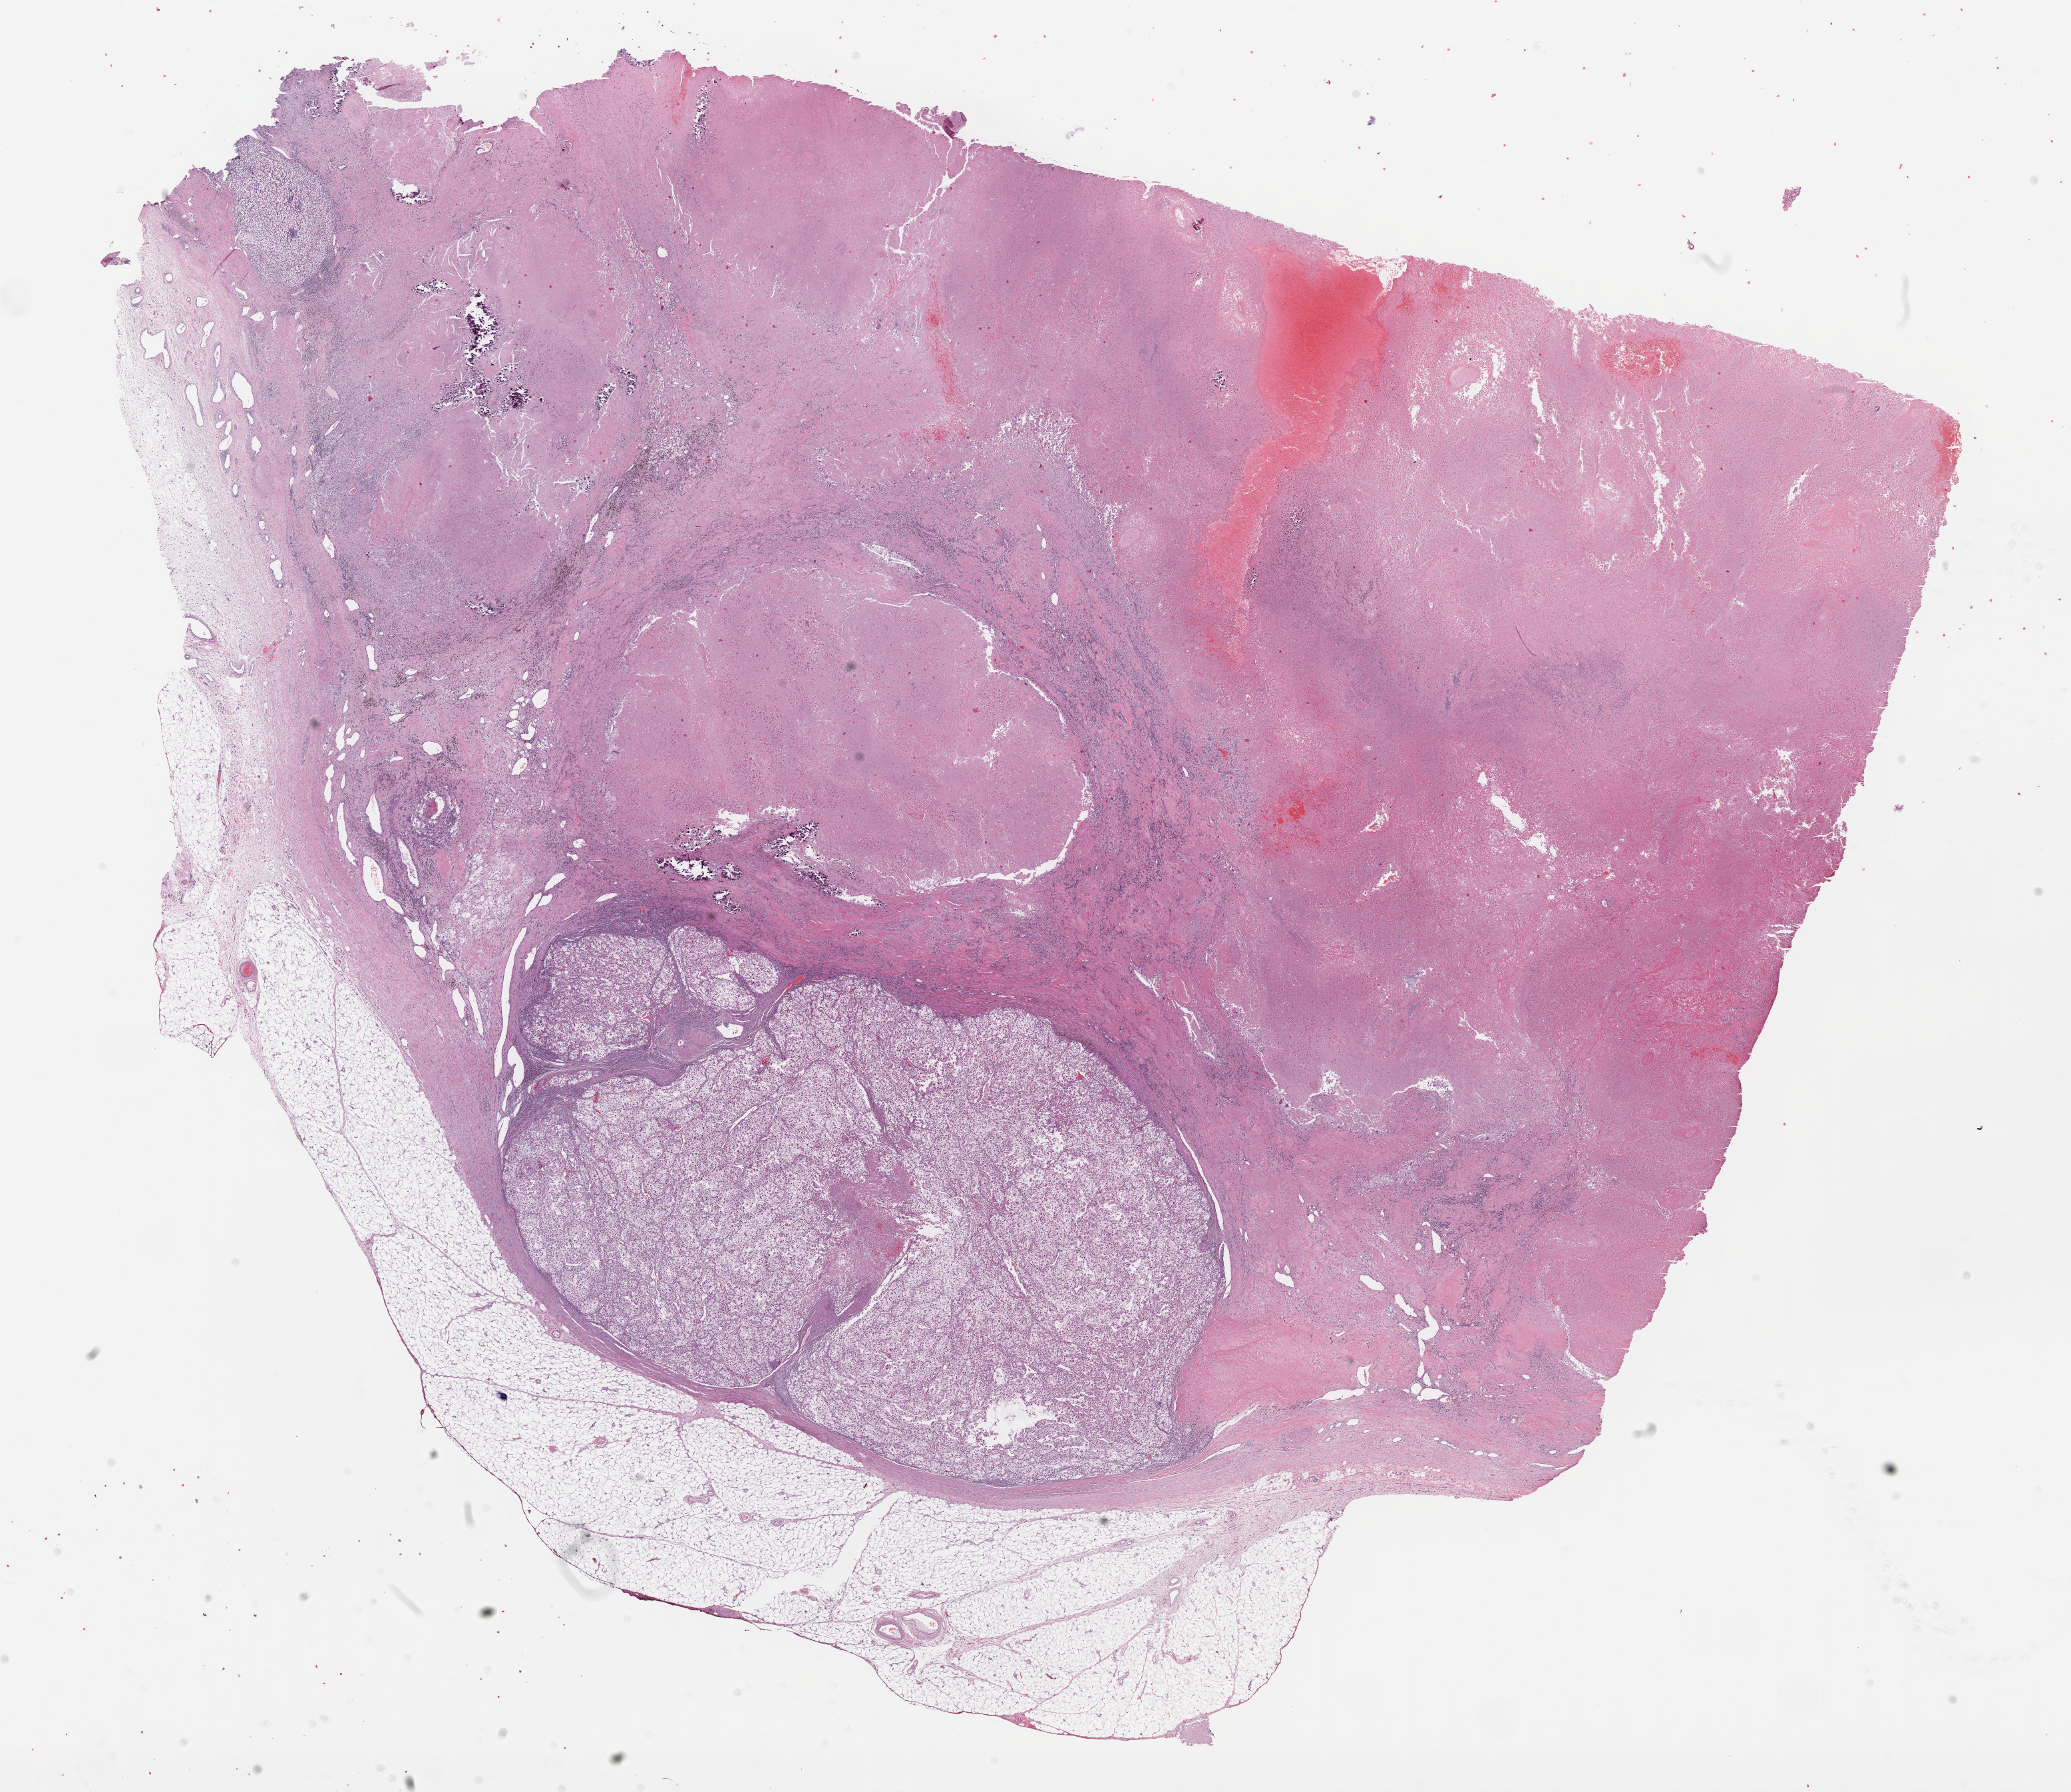
Hematoxylin and eosin (H&E) stained whole-slide image — whole scanned area (about 25.2 x 21.8 mm) shown as a low-resolution overview; formalin-fixed paraffin-embedded (FFPE) diagnostic section; primary tumour sample from the kidney. Female patient; age at initial diagnosis 81 years.
Histologic diagnosis: Clear cell adenocarcinoma, NOS.